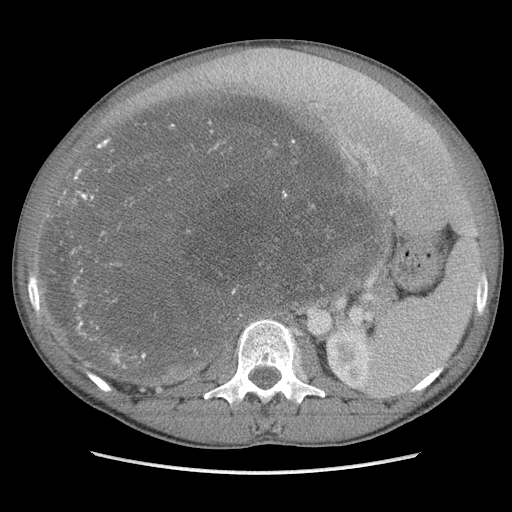
Contrast-enhanced abdominal CT, one axial slice. Position 64 of 115 along the scan axis. Soft-tissue window (W 400 / L 40 HU). 5 mm slice thickness. 512 × 512 image matrix, field of view 360 × 360 mm. Male patient. Case-level facts recorded for this patient, not image findings: diagnosis: adrenocortical carcinoma; tumour side: right adrenal; Ki-67 index: 13 %; stage (as recorded): 3.
Outlined on this slice (semi-automatically segmented with operator editing):
- mass: bounding box [x1, y1, x2, y2] px = [50, 95, 380, 382]